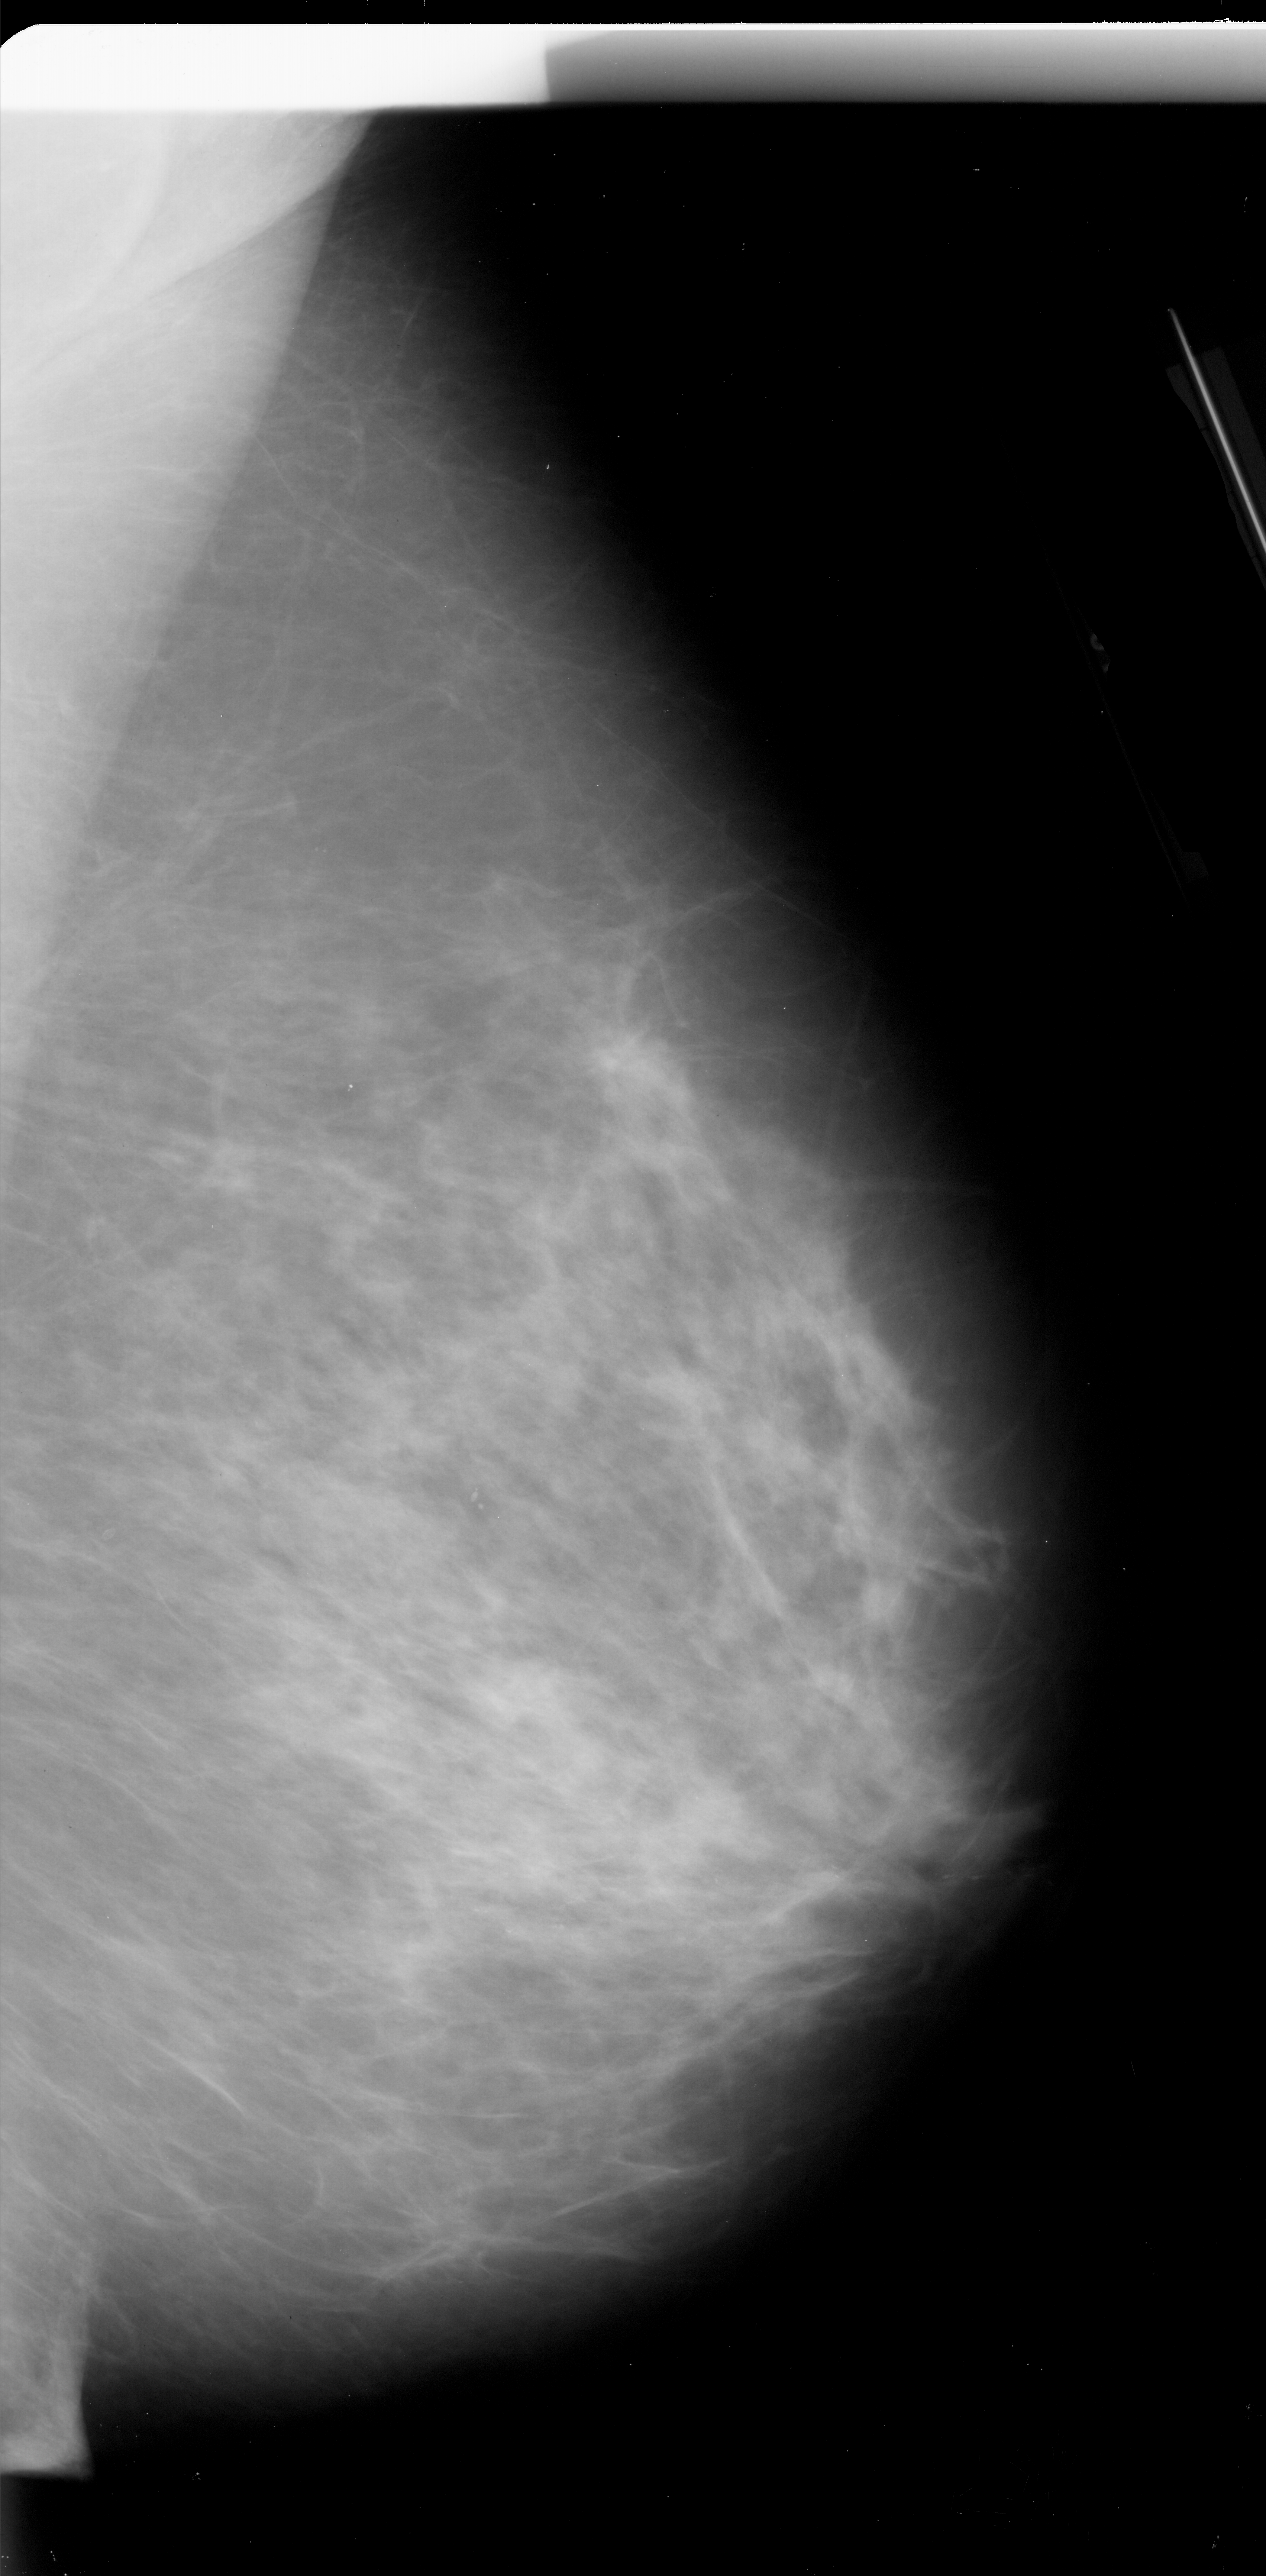
Mammogram (digitized film); right breast; mediolateral oblique (MLO) view; breast composition: heterogeneously dense (BI-RADS density category 3 of 4); 1266 × 2576 image matrix.
Expert-marked regions of interest on this image (one box per marked abnormality):
- calcifications, morphology pleomorphic, distribution linear; BI-RADS assessment category 4; pathology (as recorded): malignant: bounding box (x1, y1, x2, y2) in pixels: (456, 1873, 600, 1949)